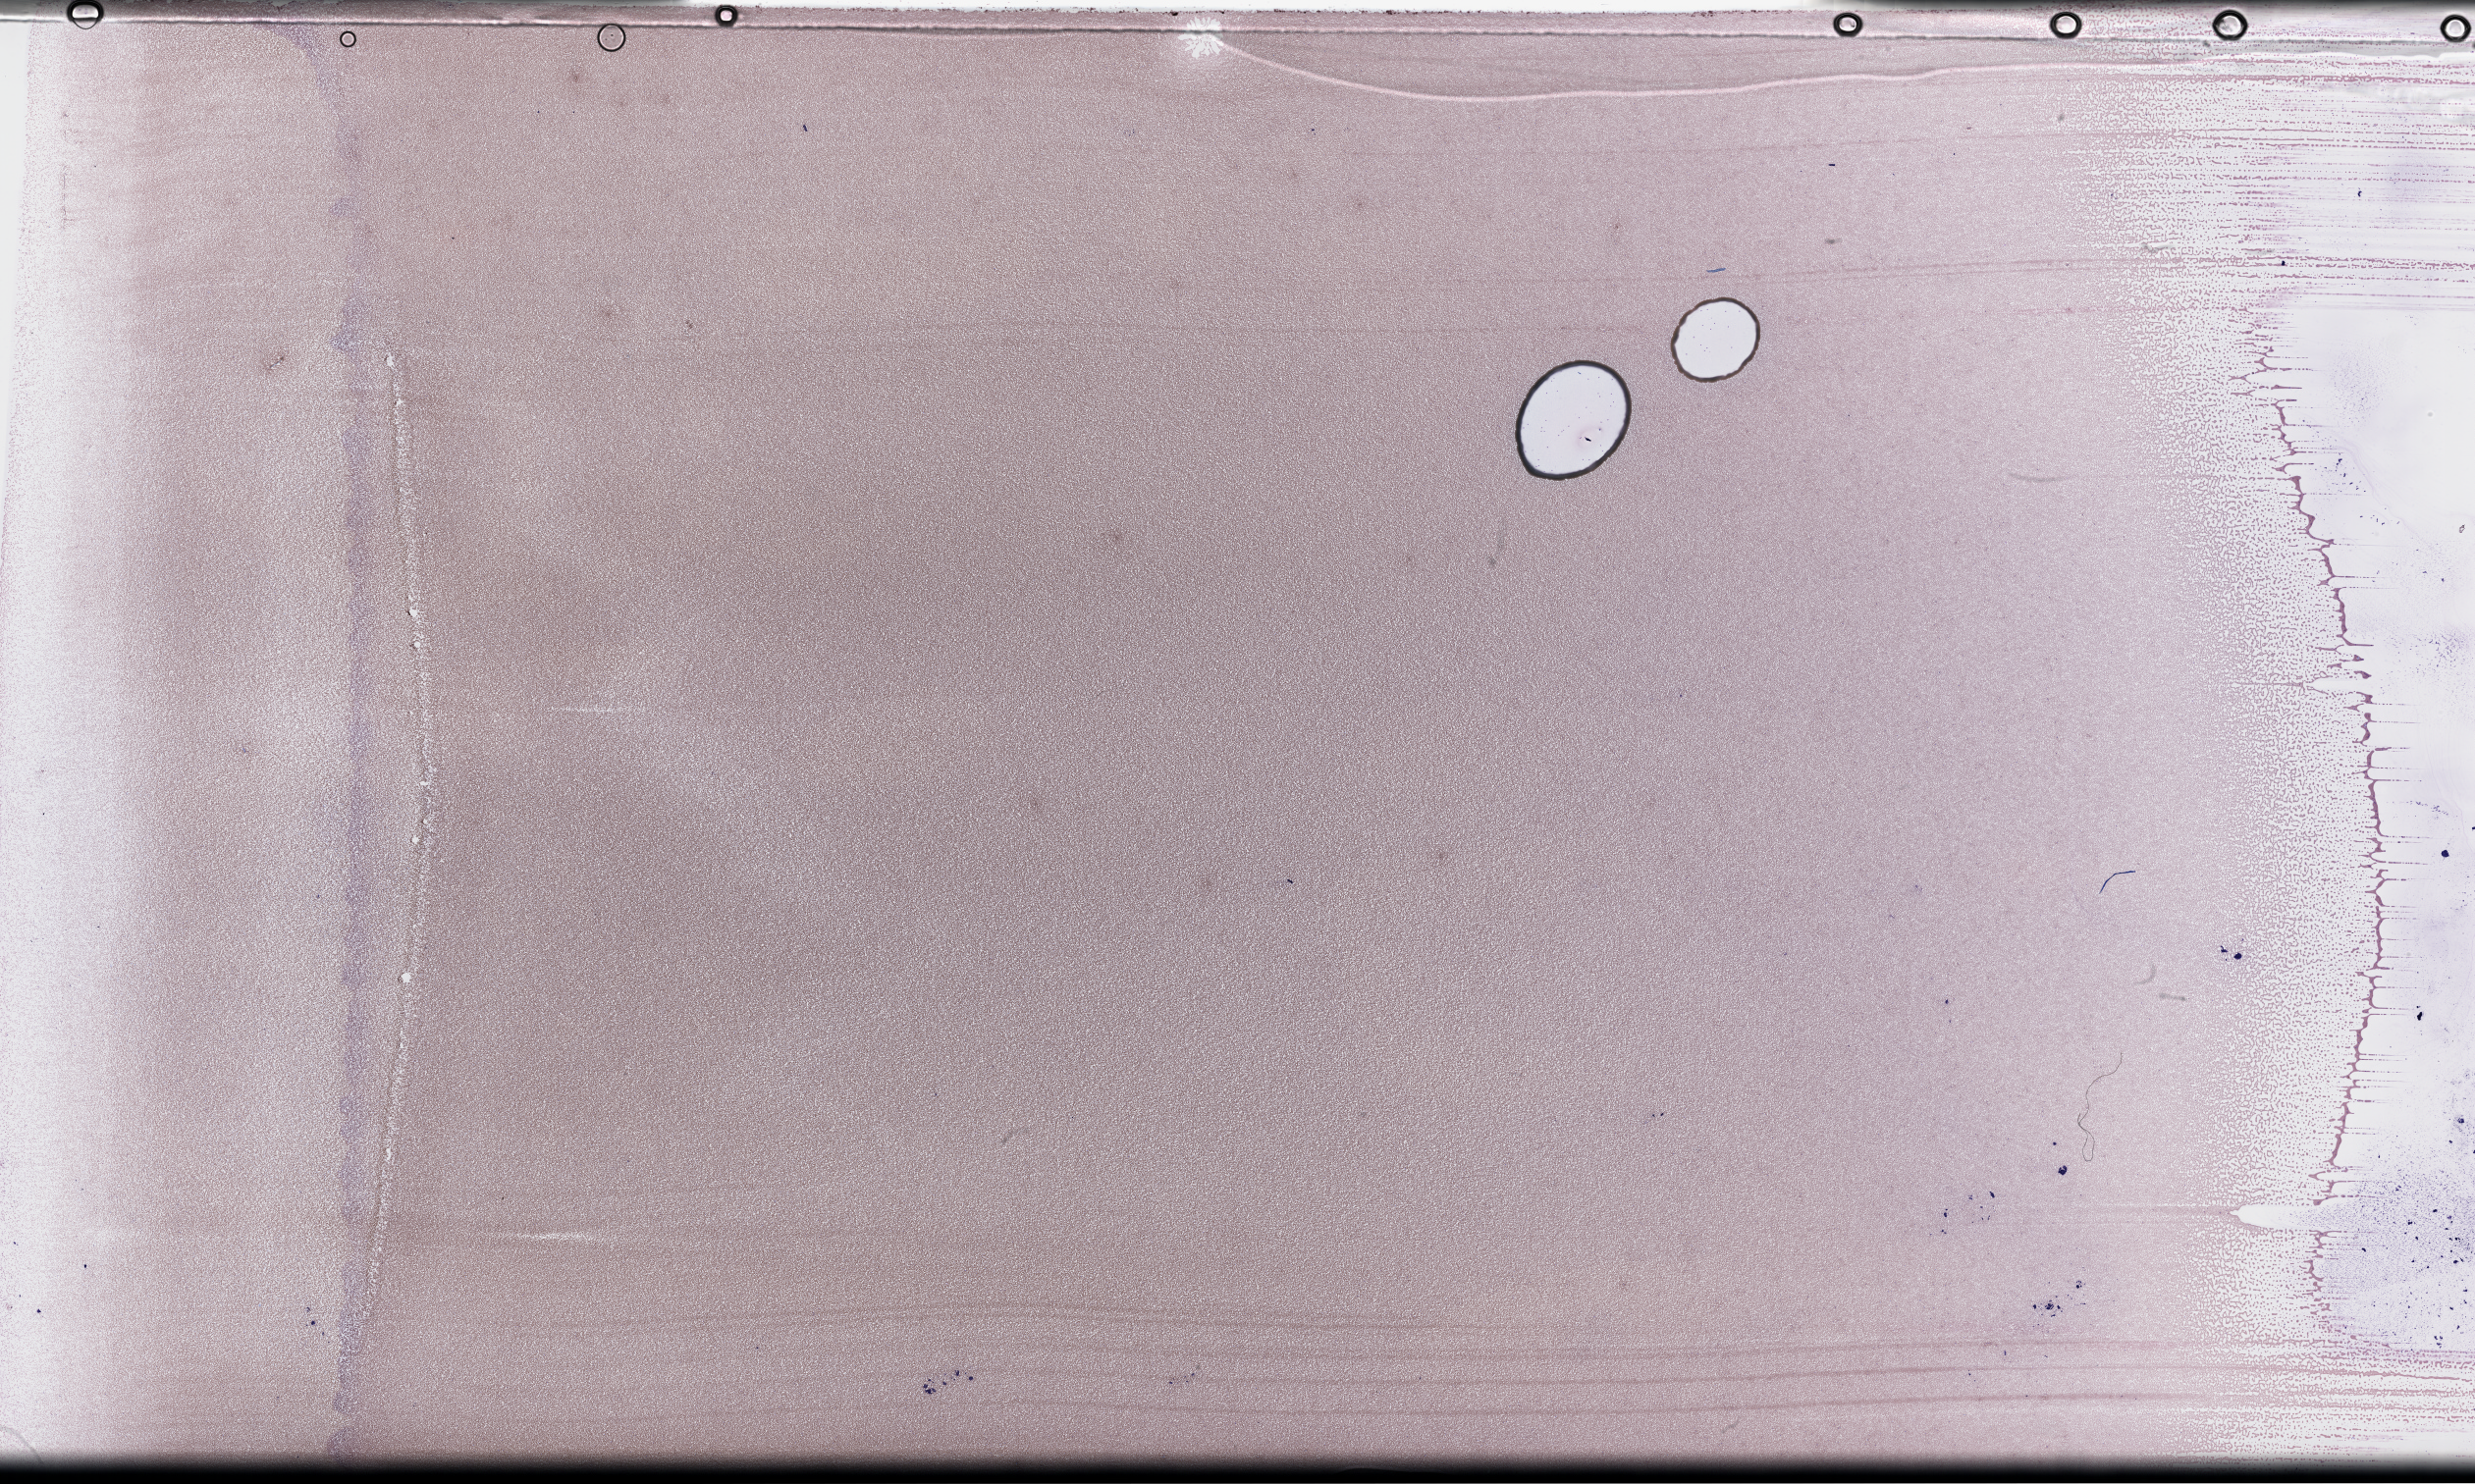
Whole-slide image of a whole blood smear, Wright-Giemsa stain, a low-resolution overview of the entire scanned area, about 40.7 x 24.4 mm. Male patient.
From a patient with: Plasma Cell Myeloma.